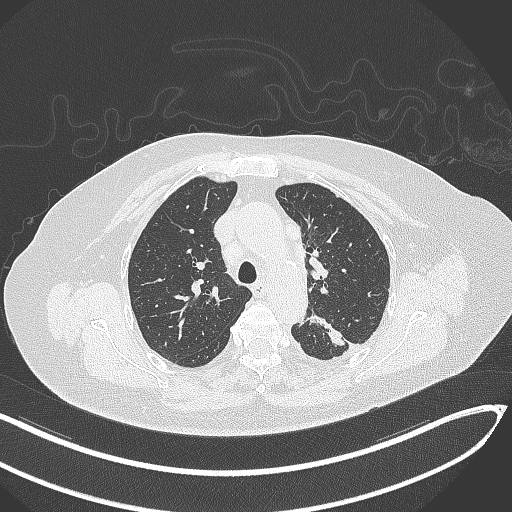
Chest CT, one axial slice. Slice 224 of 270 in the series (ordered by position). Reconstruction kernel B70f. Lung window (W 1500 / L -600 HU). 512 × 512 image matrix, field of view 400 × 400 mm. Patient: female, 76 years. Case-level facts recorded for this patient, not image findings: clinical TNM (as recorded): T1c N0 M0.
Annotated regions visible in this slice (rectangle marked by the reading radiologist):
- lung tumour (recorded histology: adenocarcinoma): bounding box [x1, y1, x2, y2] px = [303, 311, 349, 351]